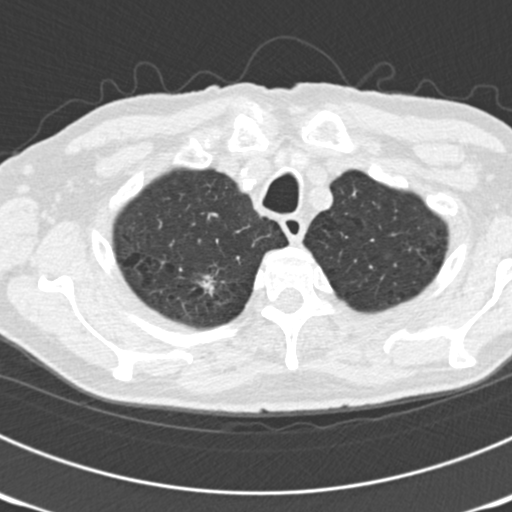
Low-dose screening chest CT, one axial slice. Position 156 of 177 along the scan axis. Reconstruction kernel B30f. 120 kVp. Lung window (W 1500 / L -600 HU). 2 mm slice thickness. 512 × 512 image matrix.
Structures marked on this image (outlined manually by an expert reader):
- lesion 3 (nodule, upper lobe of right lung): bounding box [x1, y1, x2, y2] px = [199, 275, 219, 297]